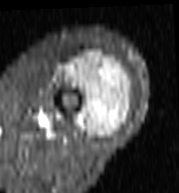
MRI of an extremity soft-tissue mass, one axial slice. STIR. MR volume resampled by the dataset authors to the PET/CT grid (not the native acquisition matrix). 3.27 mm slice thickness. 179 × 193 image matrix, field of view 175 × 188 mm. Female patient. From the clinical record (not read from this slice): histological type: undifferentiated – high grade; grade: high; site of the primary tumour: left thigh.
Outlined on this slice (expert contour drawn on MRI and transferred to this co-registered scan by the dataset authors):
- gross tumour volume including surrounding oedema: bounding box [x1, y1, x2, y2] px = [57, 53, 133, 138]
- gross tumour volume (mass): [72, 53, 131, 138]